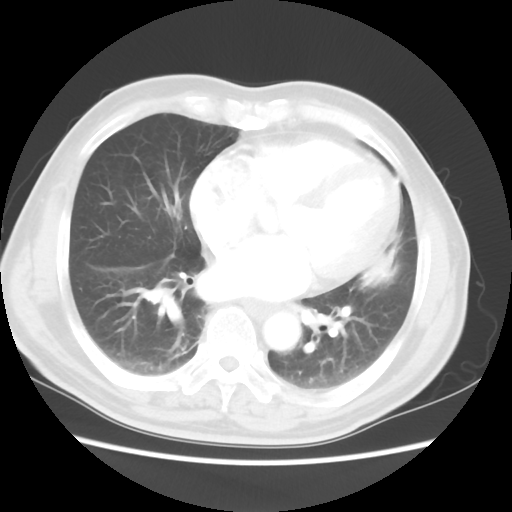
Chest CT, one axial slice; slice 19 of 50 in the series (ordered by position); reconstruction kernel STANDARD; lung window (W 1500 / L -600 HU); 5 mm slice thickness; 512 × 512 image matrix, field of view 360 × 360 mm. Male patient, age 69 years. Case-level facts recorded for this patient, not image findings: clinical TNM (as recorded): T3 N1 M1a.
Structures marked on this image (bounding box drawn by a radiologist):
- lung tumour (recorded histology: squamous cell carcinoma): bounding box [x1, y1, x2, y2] px = [360, 236, 409, 296]